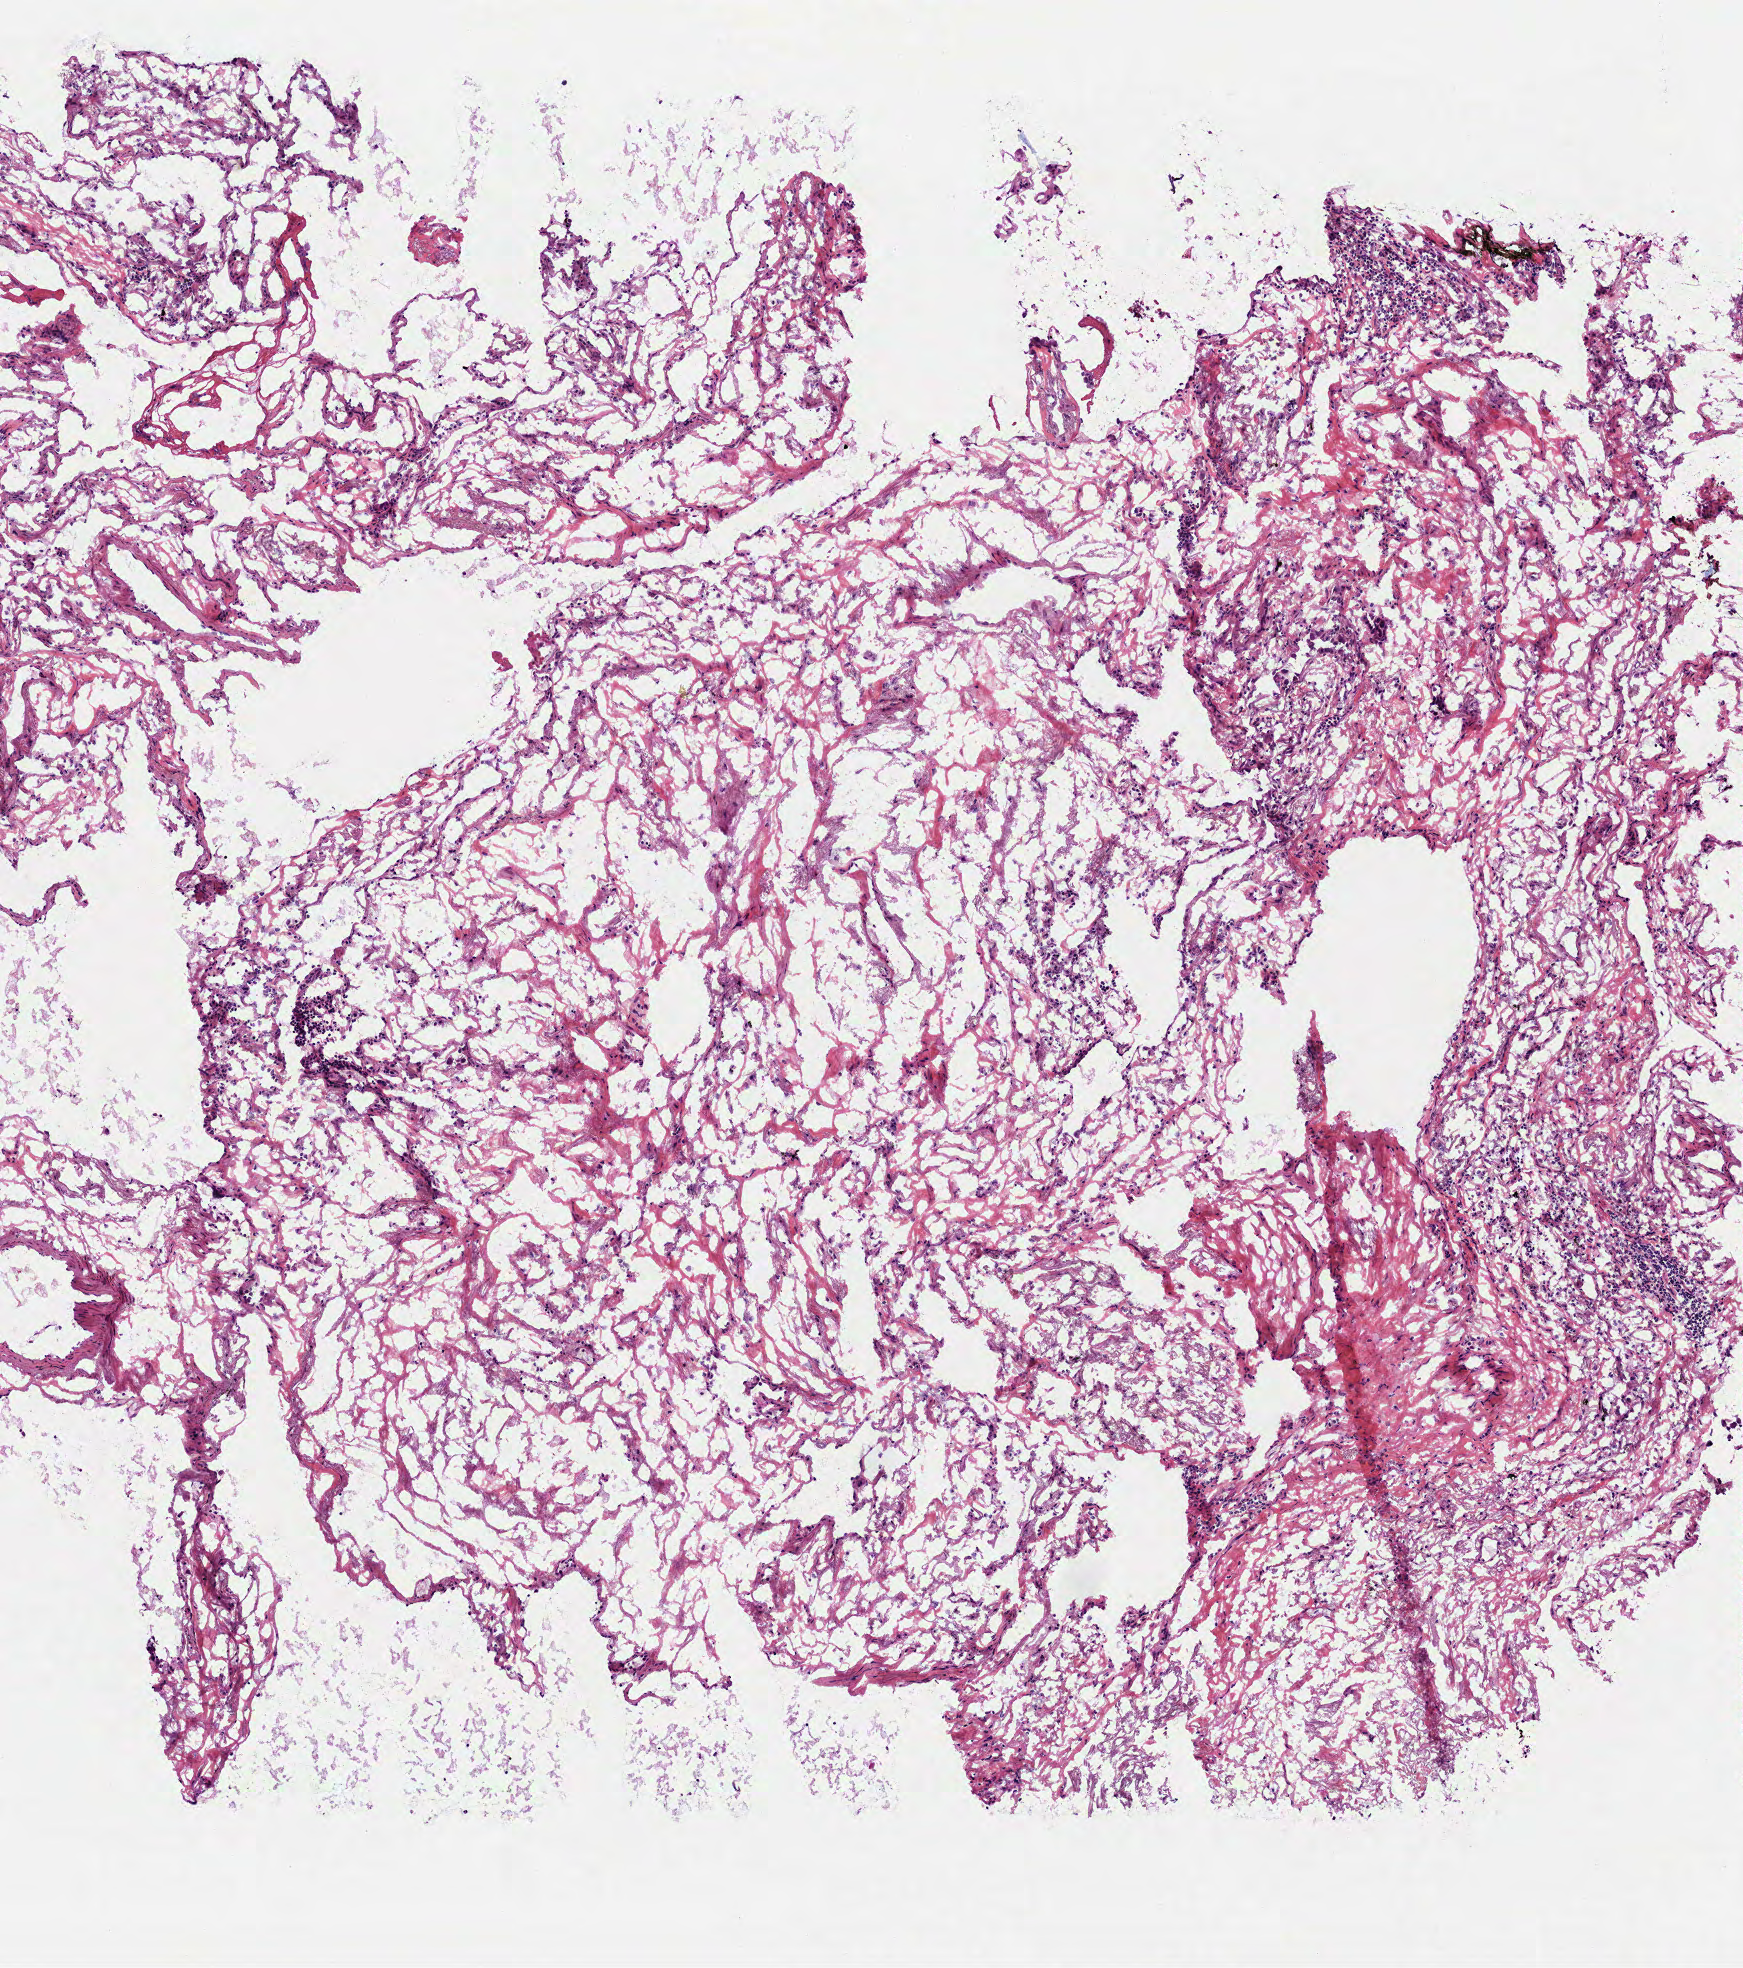
Digitized Hematoxylin and eosin (H&E) stained tissue section (whole slide), whole scanned area (about 3.5 x 4.0 mm, from a 40x scan) shown as a low-resolution overview. Frozen section from the top of the tissue portion. Primary tumour sample from the lung. Female, age 76 years at initial diagnosis. Pathologist review of this section (percent, as recorded): tumour cells 100%, tumour nuclei 67%, normal cells 0%, stromal cells 0%, necrosis 0%. Infiltration values recorded for this section: lymphocyte infiltration 25%, monocyte infiltration 5%, neutrophil infiltration 0%.
Histologic diagnosis: Squamous cell carcinoma, NOS (lower lobe, lung). AJCC pathologic stage: IB (7th edition).